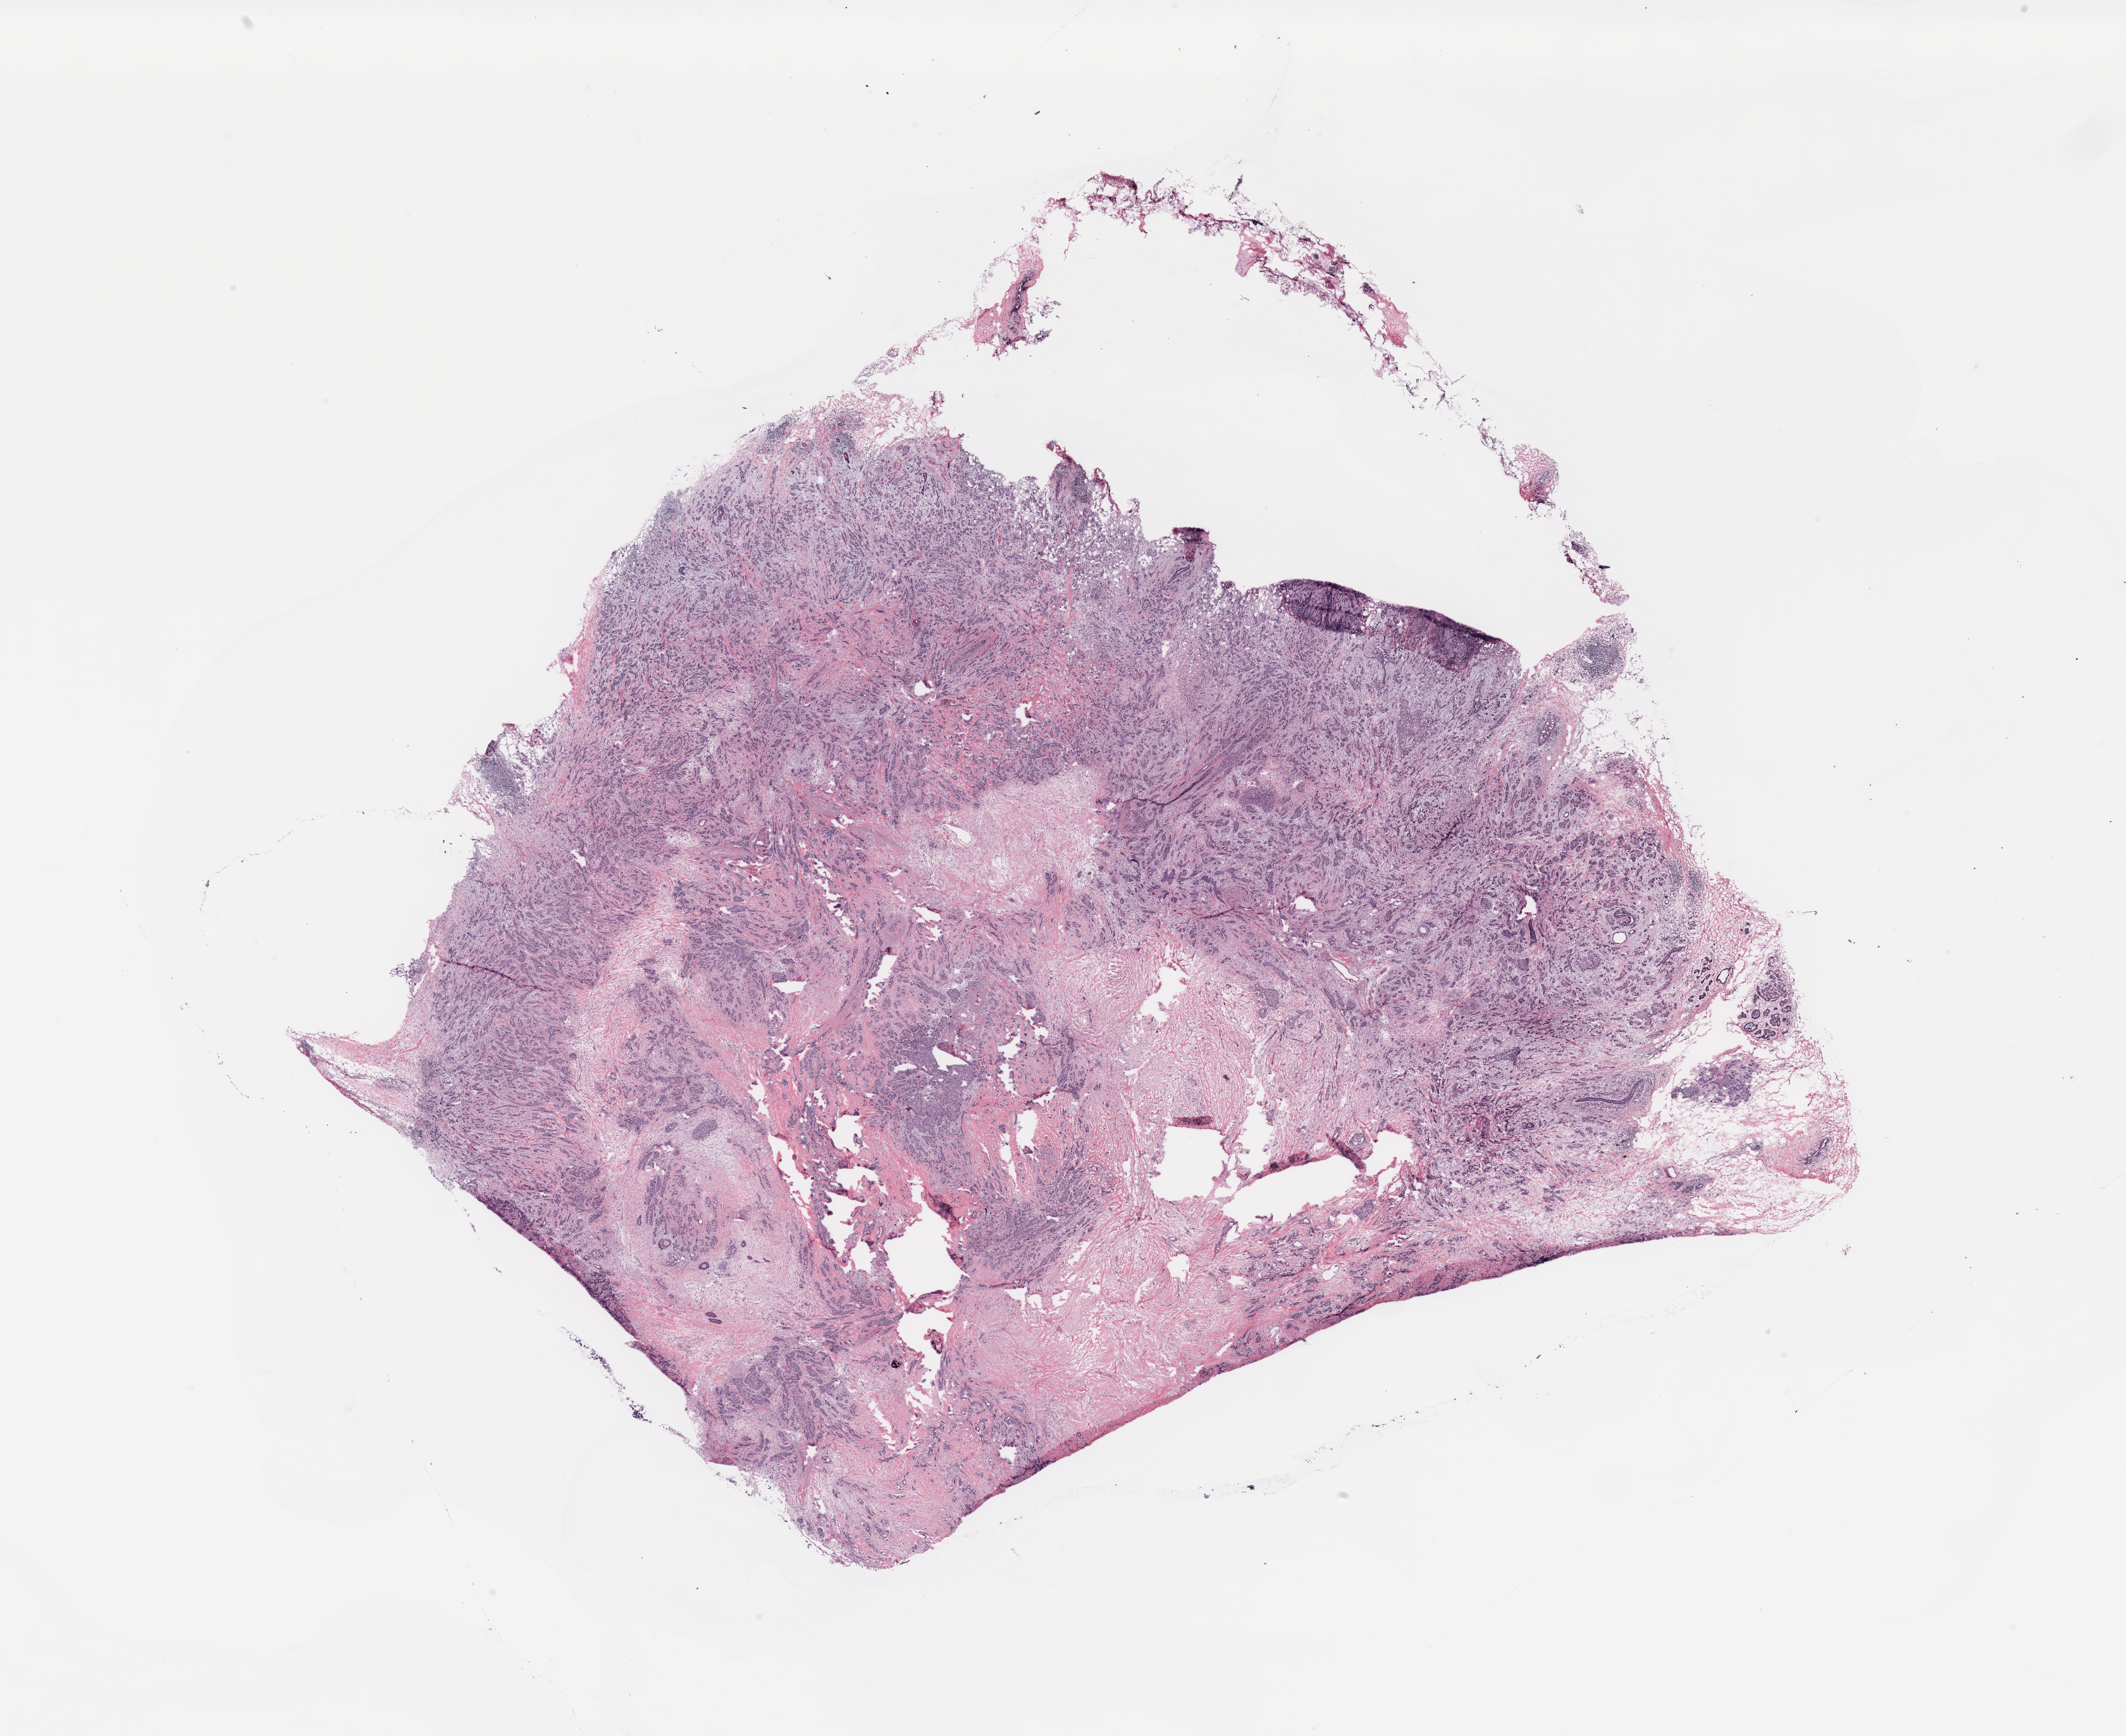
Whole-slide histology image, H&E-stained, shown as a low-resolution overview of the whole scanned area (about 26.6 x 21.7 mm, slide scanned at 20x), breast, tissue type not recorded.
Patient diagnosis (cohort enrolment): breast cancer (breast).